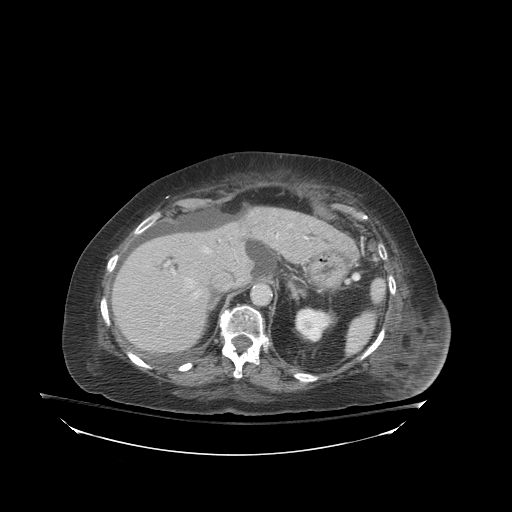
Contrast-enhanced abdominal CT (liver protocol), one axial slice. Reconstruction kernel STANDARD. 140 kVp. Soft-tissue window (W 400 / L 40 HU). 512 × 512 image matrix, field of view 500 × 500 mm. Case-level facts recorded for this patient, not image findings: diagnosis: hepatocellular carcinoma (patient treated with transarterial chemoembolisation; whether this scan precedes or follows treatment is not stated here); TNM stage (as recorded): Stage-I; Child-Pugh class: B; tumour differentiation: well-moderately differentiated; tumour nodularity: uninodular.
Outlined on this slice (semi-automatically segmented with operator editing):
- liver parenchyma outside the tumour (the mass and vessels are separate outlines, so this box may not span the whole liver): bounding box <112,206,356,352> (left, top, right, bottom; pixels)
- liver vessels: <166,234,307,297>